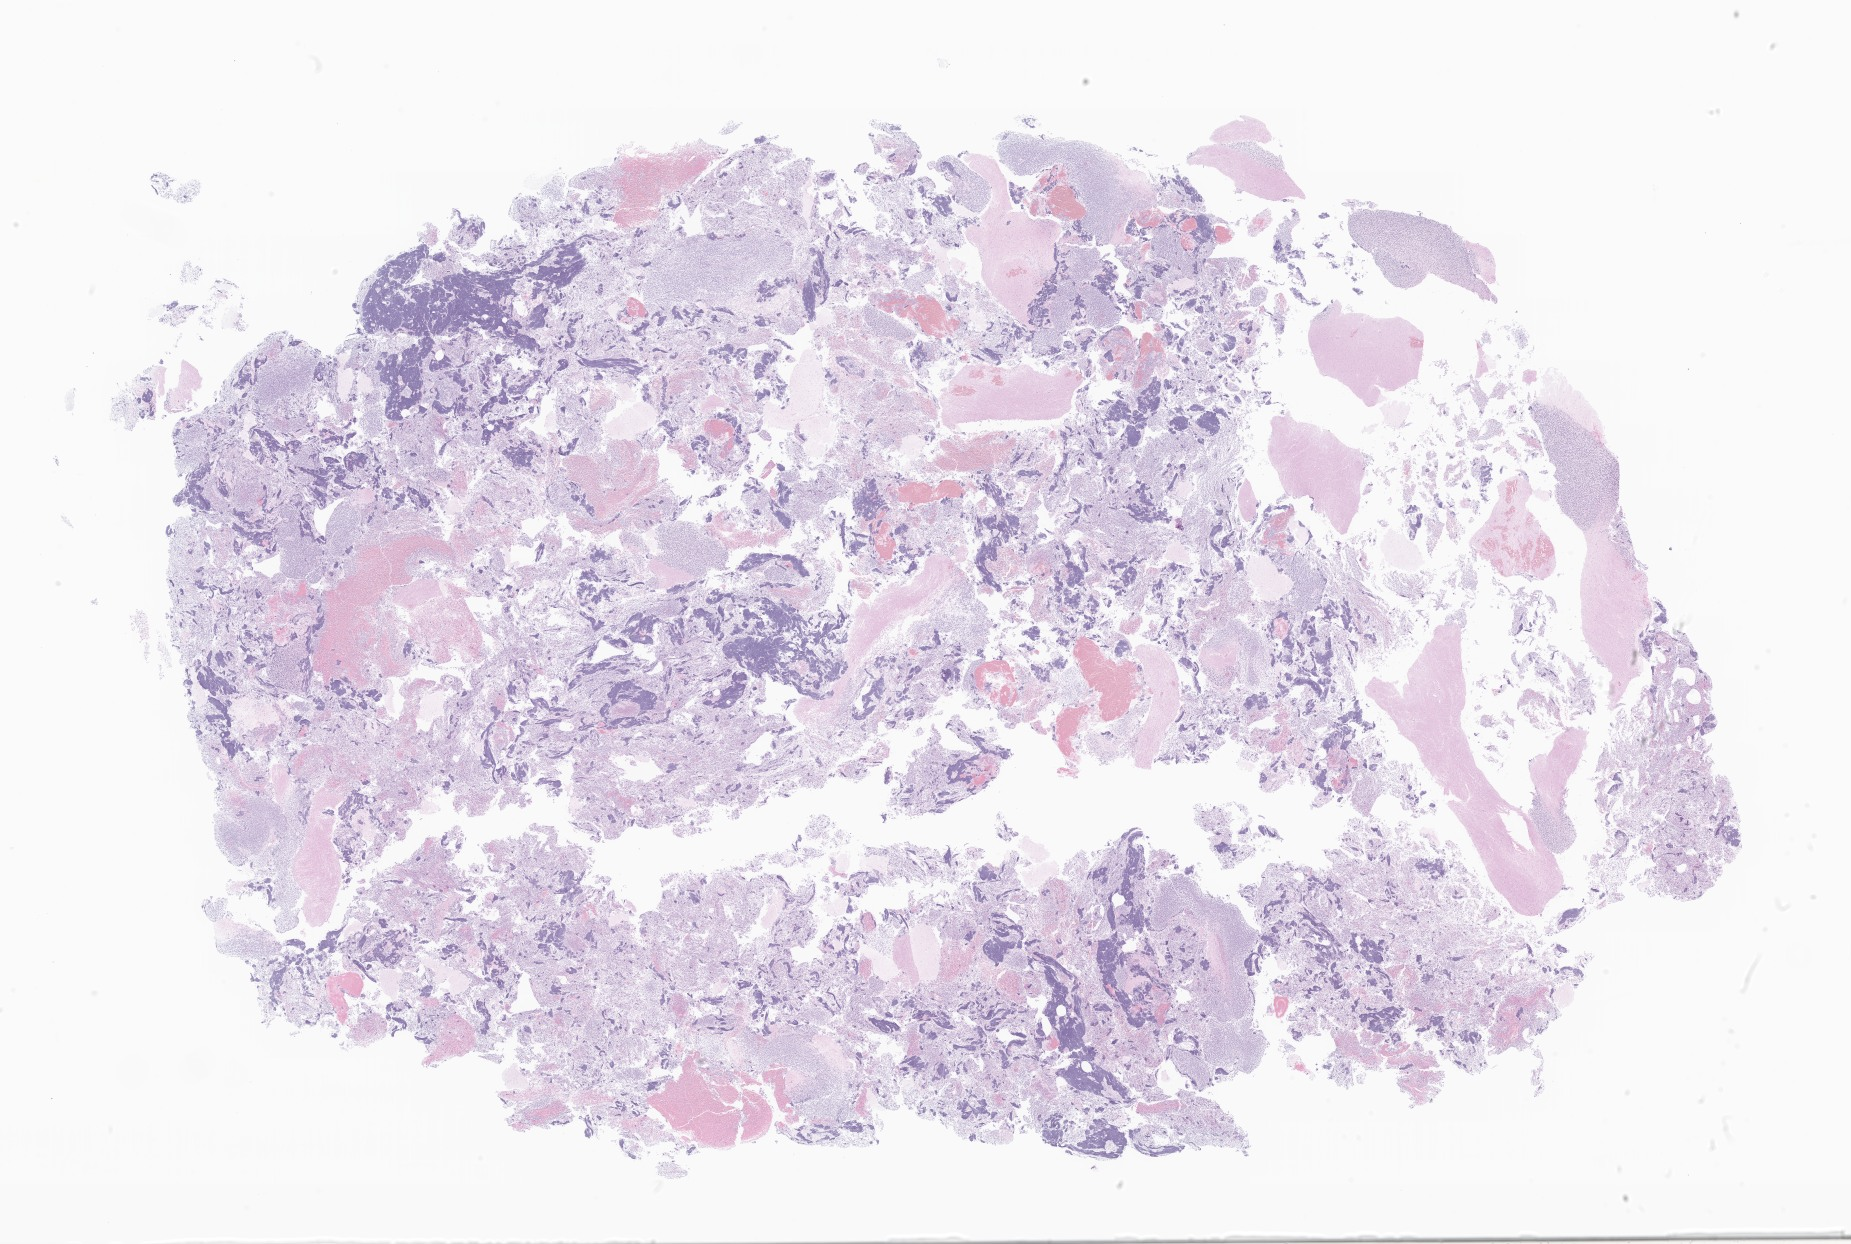
Digitized haematoxylin and eosin-stained section of tumor tissue from the cerebellum — a low-resolution overview of the entire scanned area, about 31.2 x 21.0 mm; FFPE section. Female patient, age 43 months (3 years 7 months).
Diagnosis: Neoplasm, malignant.